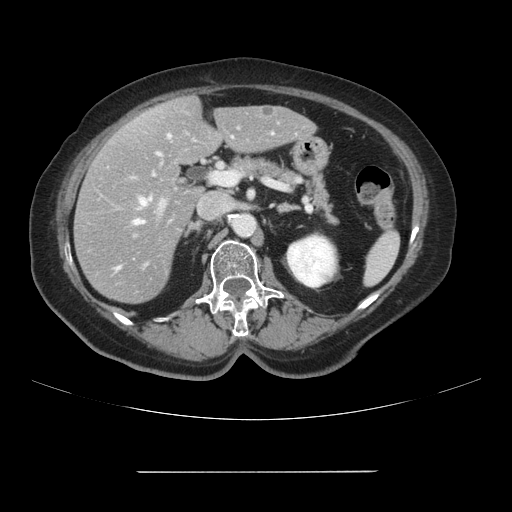
Contrast-enhanced abdominal CT, one axial slice; position 50 of 111 along the scan axis; intravenous contrast given; soft-tissue window (W 400 / L 40 HU); 2.5 mm slice thickness; 512 × 512 image matrix, field of view 400 × 400 mm. Female patient, age 74 years. Case-level facts recorded for this patient, not image findings: diagnosis: colorectal cancer liver metastases, imaged before liver resection; multiple liver metastases: yes; largest metastasis: 1.1 cm.
Annotated regions visible in this slice (outlined manually by an expert reader):
- hepatic veins: bounding box (x1, y1, x2, y2) in pixels: (134, 136, 170, 225)
- liver: (75, 97, 315, 303)
- planned liver remnant (the part of the liver to remain after resection): (143, 97, 315, 165)
- portal vein (with intrahepatic branches): (131, 120, 281, 217)
- liver metastasis: (261, 106, 271, 114)